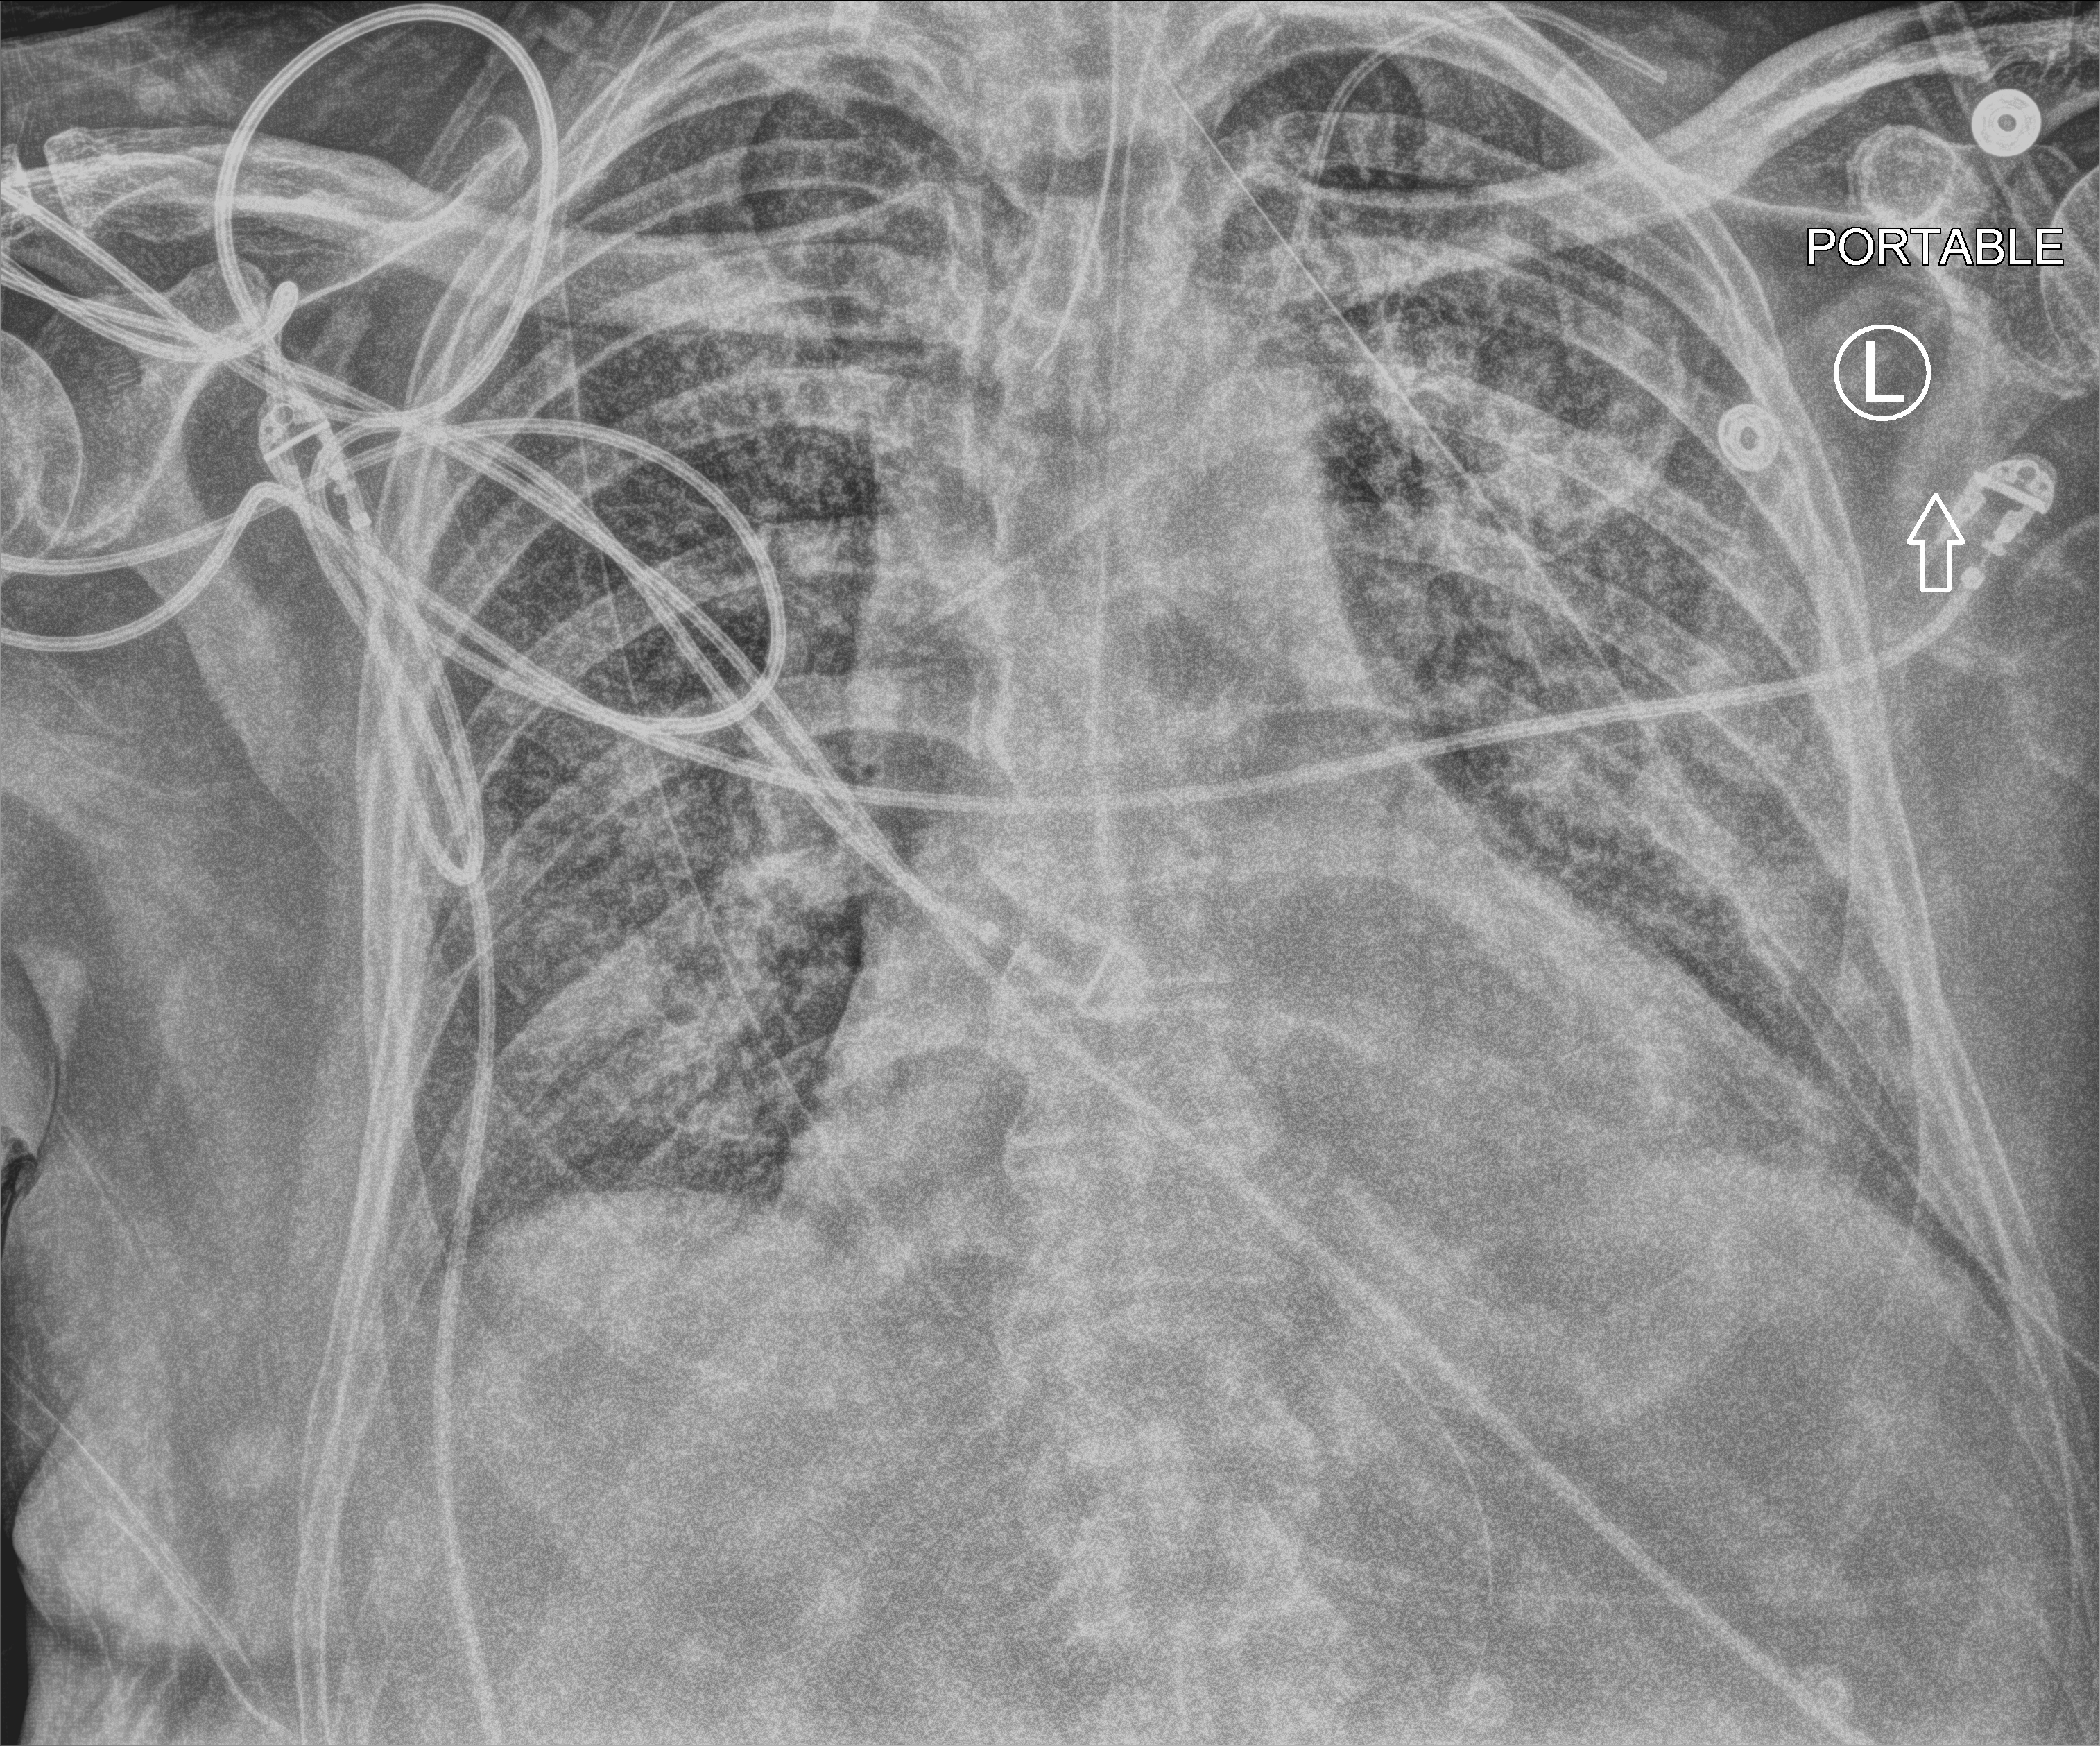
Portable chest radiograph, anteroposterior (AP) projection. Male patient hospitalised with COVID-19, age 75–90 years.
Hospital-stay facts (about this admission, not read from this image; timing relative to this image not recorded): admitted to intensive care during this hospital stay: yes; chronic kidney disease (admission record): no; mechanically ventilated during this hospital stay: yes.